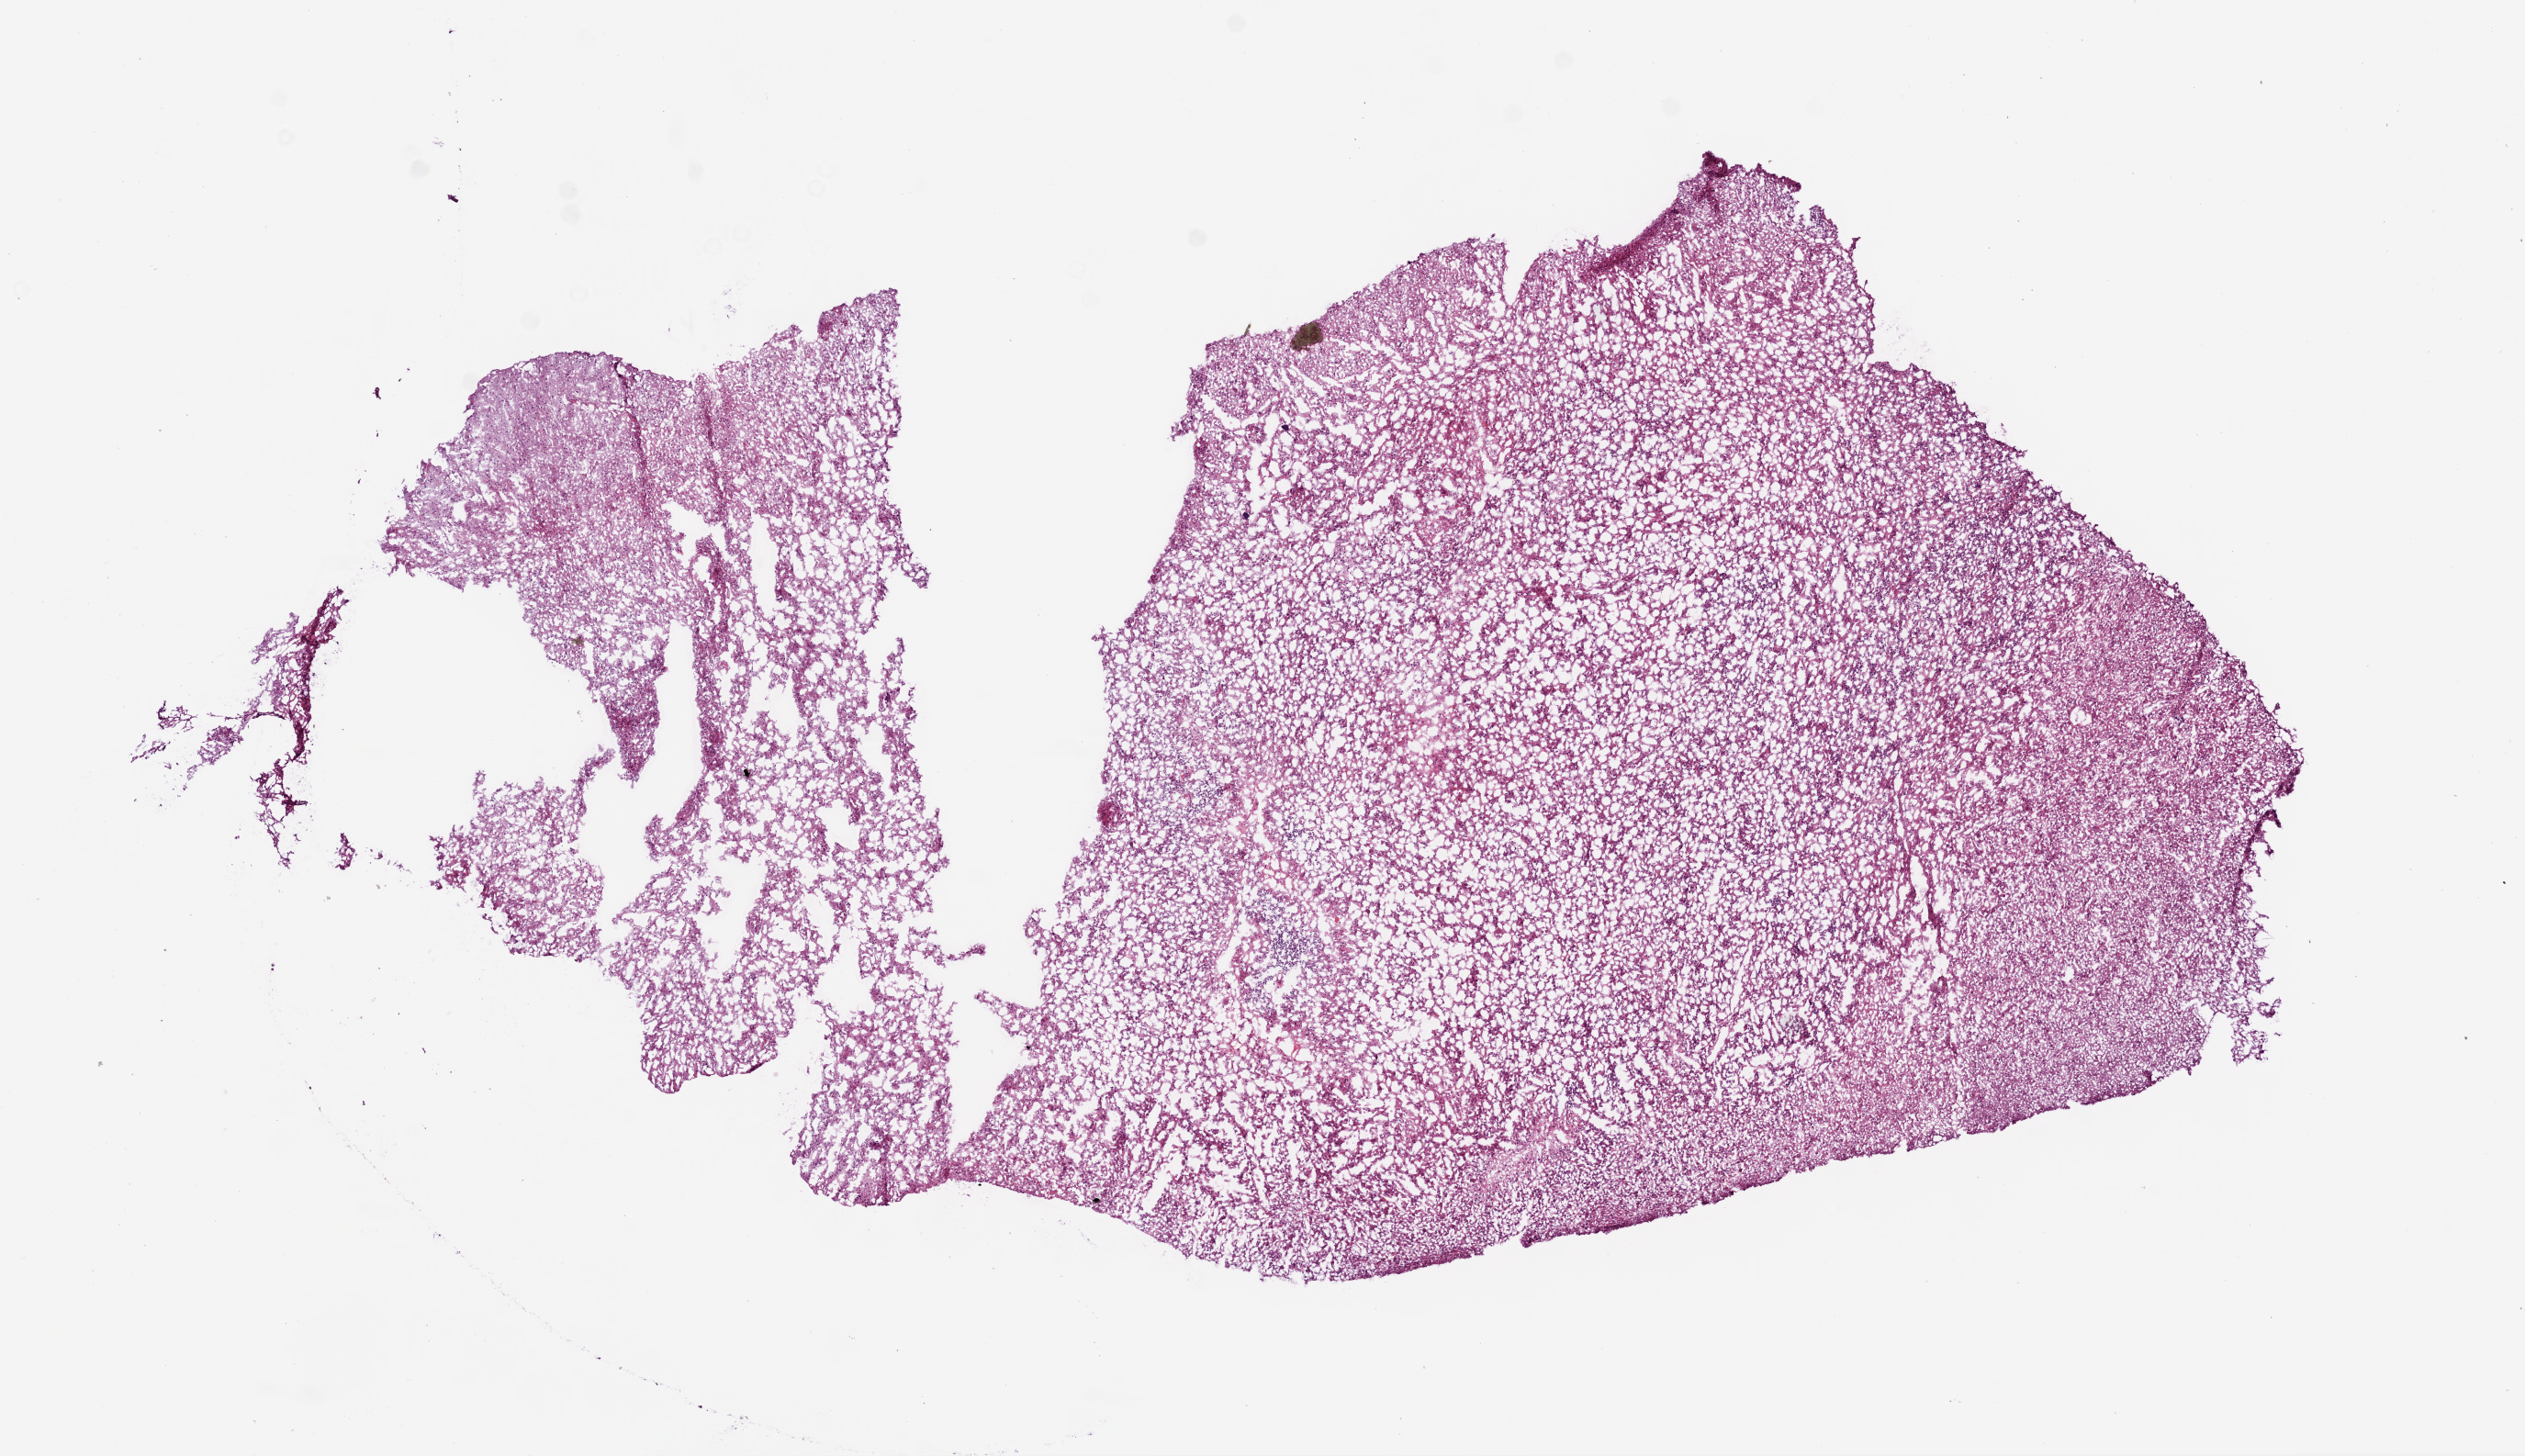
Whole-slide histology image, H&E-stained, shown as a low-resolution overview of the whole scanned area (about 11.0 x 6.4 mm, acquisition: 20x scan), frozen section from the bottom of the tissue portion, sample: primary tumour, brain. Female, age 78 years at initial diagnosis. Slide review estimates, as recorded: tumour cells 100%, tumour nuclei 80%, normal cells 0%, stromal cells 0%, necrosis 0%.
Diagnosis: Glioblastoma.